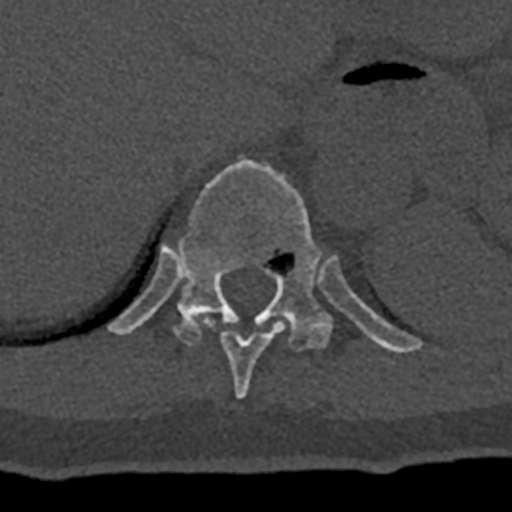
CT including the spine, one axial slice. Slice 568 of 797 in the series (ordered by position). 120 kVp. Bone window (W 1800 / L 400 HU). 512 × 512 image matrix. Male patient, age 74 years. Case-level facts recorded for this patient, not image findings: primary cancer: renal; vertebrae with lytic lesions (as recorded): T10, L1, L2, L3, L4, L5.
Structures marked on this image (semi-automatically segmented with operator editing):
- T10 vertebra: bounding box <199,318,286,399> (left, top, right, bottom; pixels)
- T11 vertebra: <107,157,424,354>